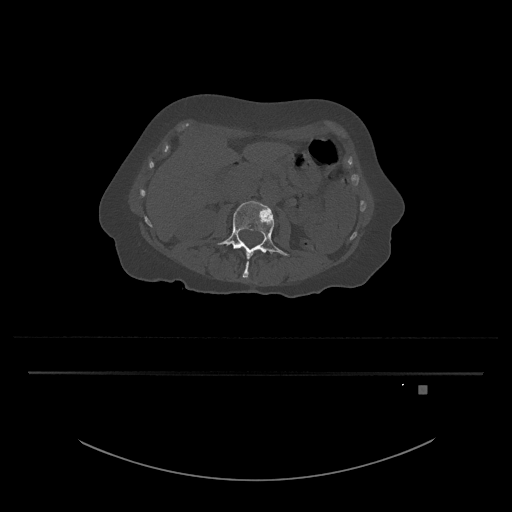
CT including the spine, one axial slice. Slice 432 of 797 in the series (ordered by position). Reconstruction kernel Br40s/3. Bone window (W 1800 / L 400 HU). 0.5 mm slice thickness. 512 × 512 image matrix, field of view 500 × 500 mm. Female patient, age 57 years. From the clinical record (not read from this slice): primary cancer: cervical.
Annotated regions visible in this slice (semi-automatic segmentation, software-assisted and operator-edited):
- L3 vertebra: box from (x=217, y=201) to (x=290, y=278) px